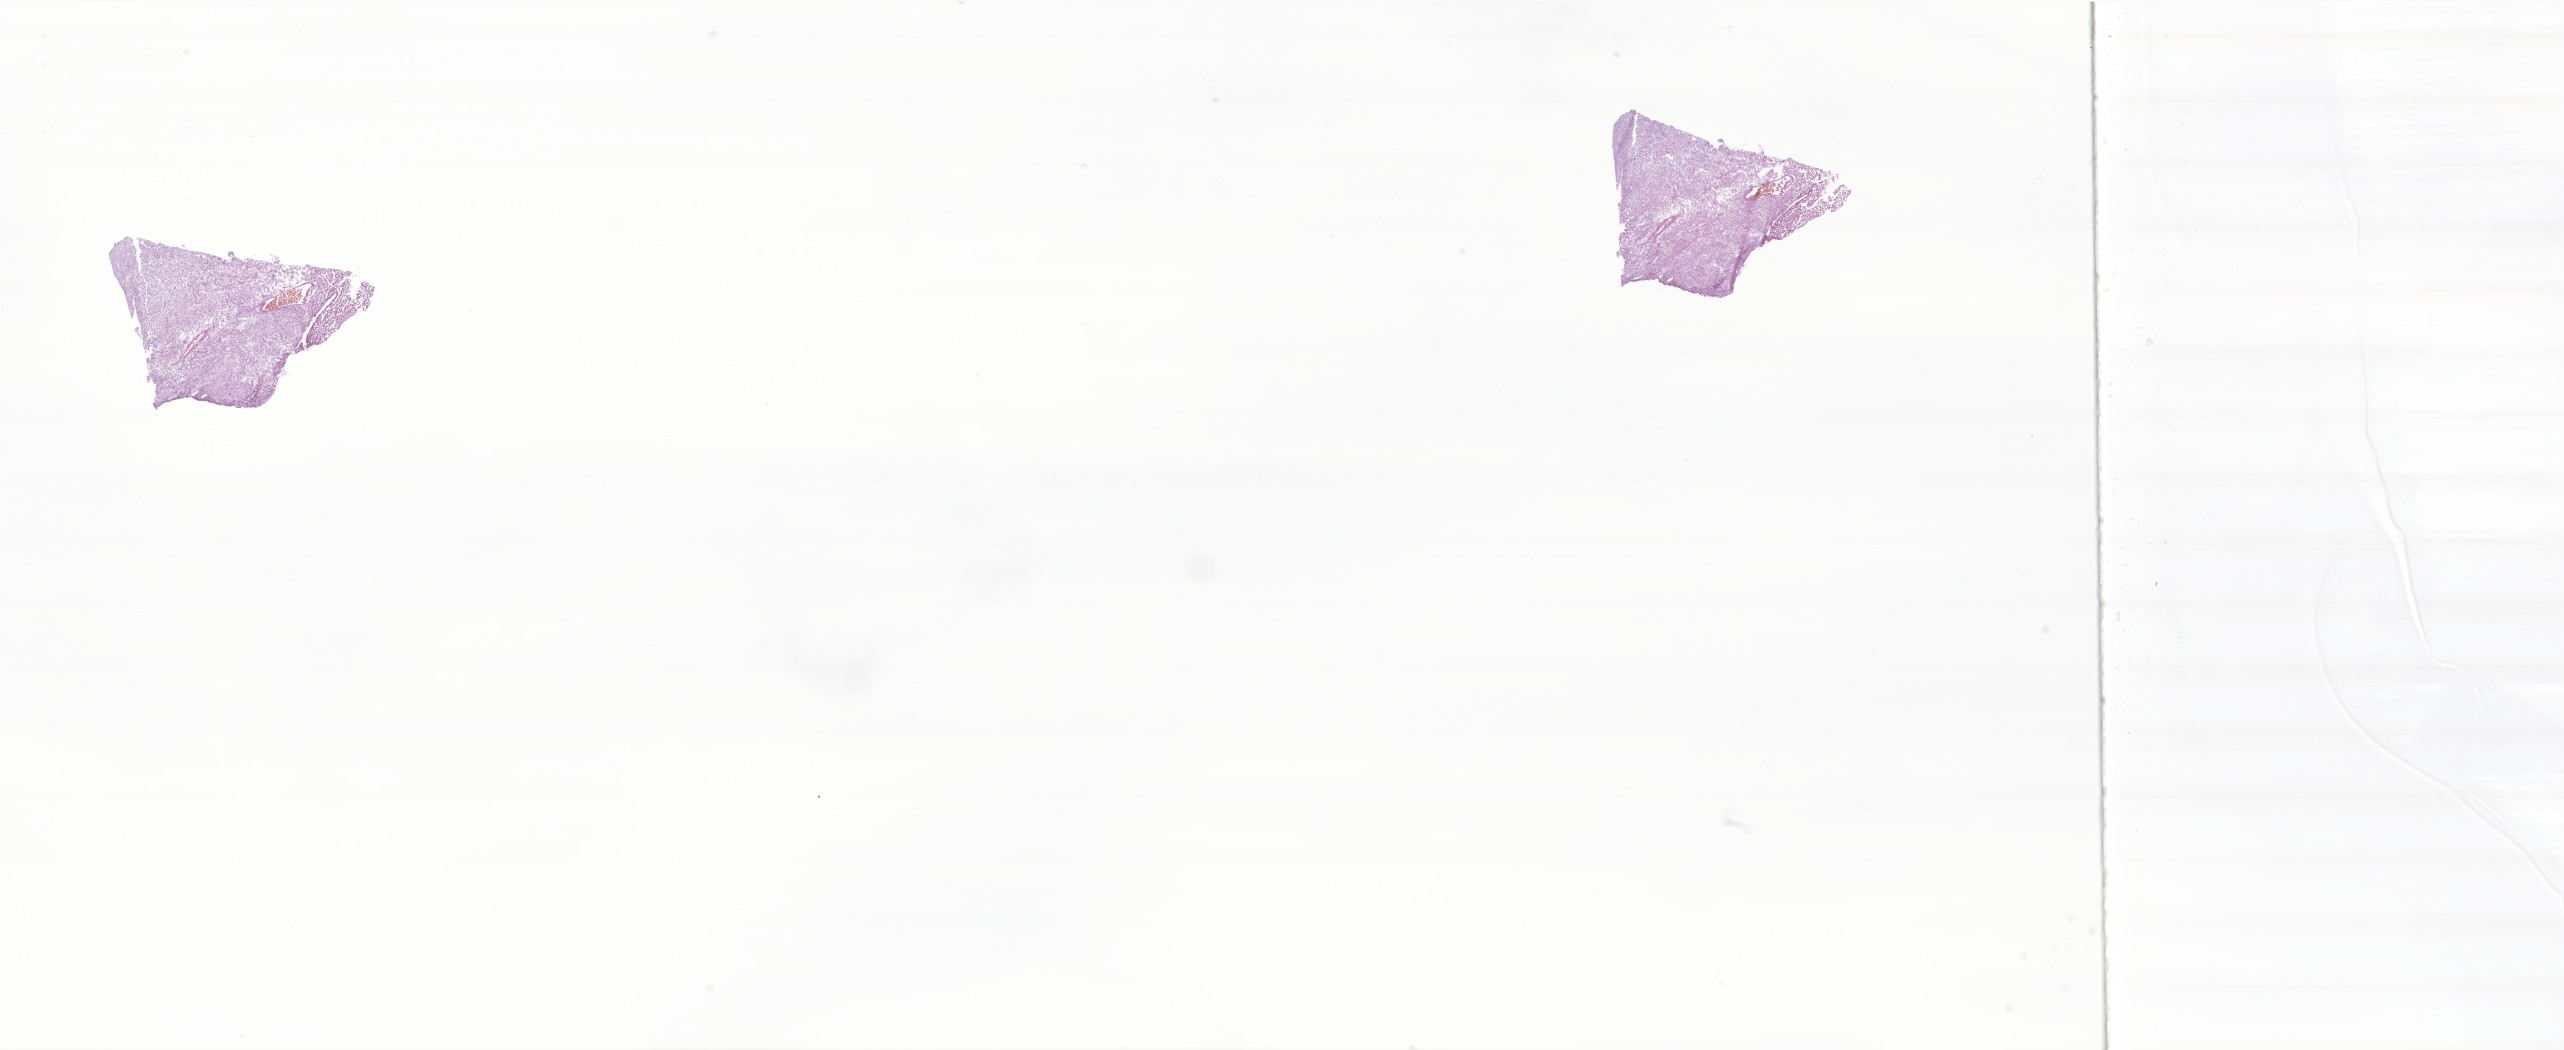
Hematoxylin and eosin (H&E) whole-slide image of tumor tissue from the frontal lobe — low-resolution overview of the scanned area, about 43.2 x 17.7 mm; frozen section. Patient female; age 48 months.
* diagnosis: Meningioma, NOS